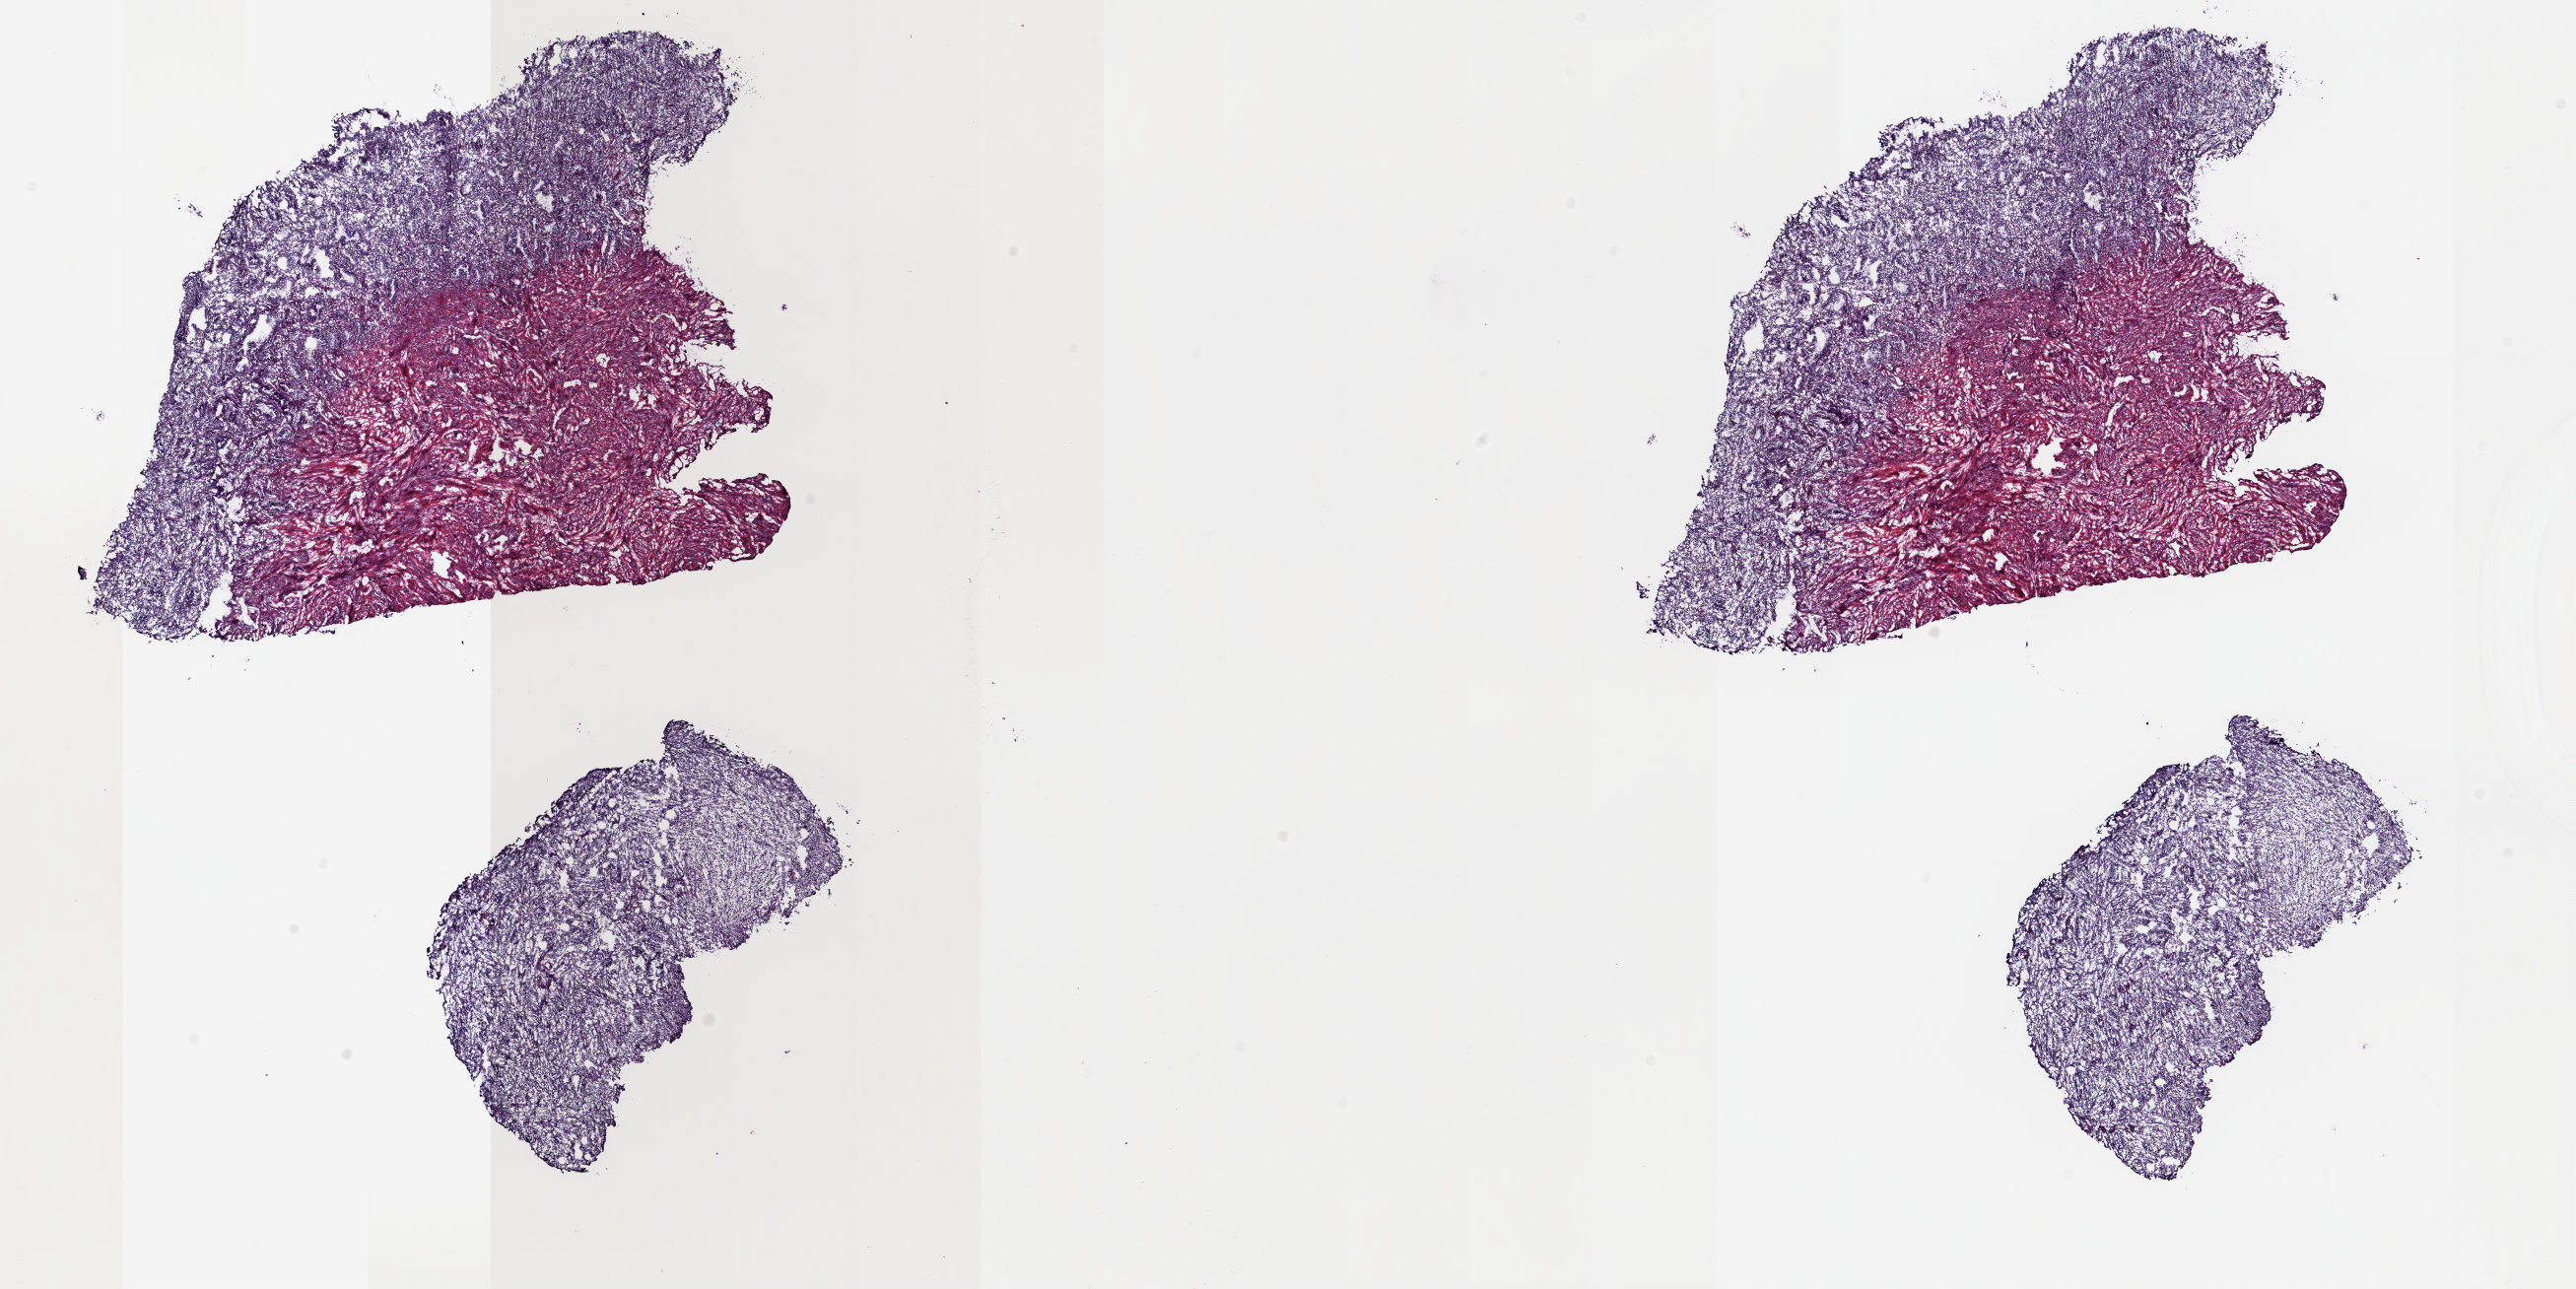
Whole-slide histology image, H&E-stained — whole scanned area (about 20.8 x 10.4 mm, acquisition: 20x scan) shown as a low-resolution overview, frozen section, sample: solid tissue normal (non-tumour tissue), uterus. Composition of this section per pathologist review: tumour cells 0%, normal cells 100%.
This section: solid tissue normal sample (biorepository sample class).